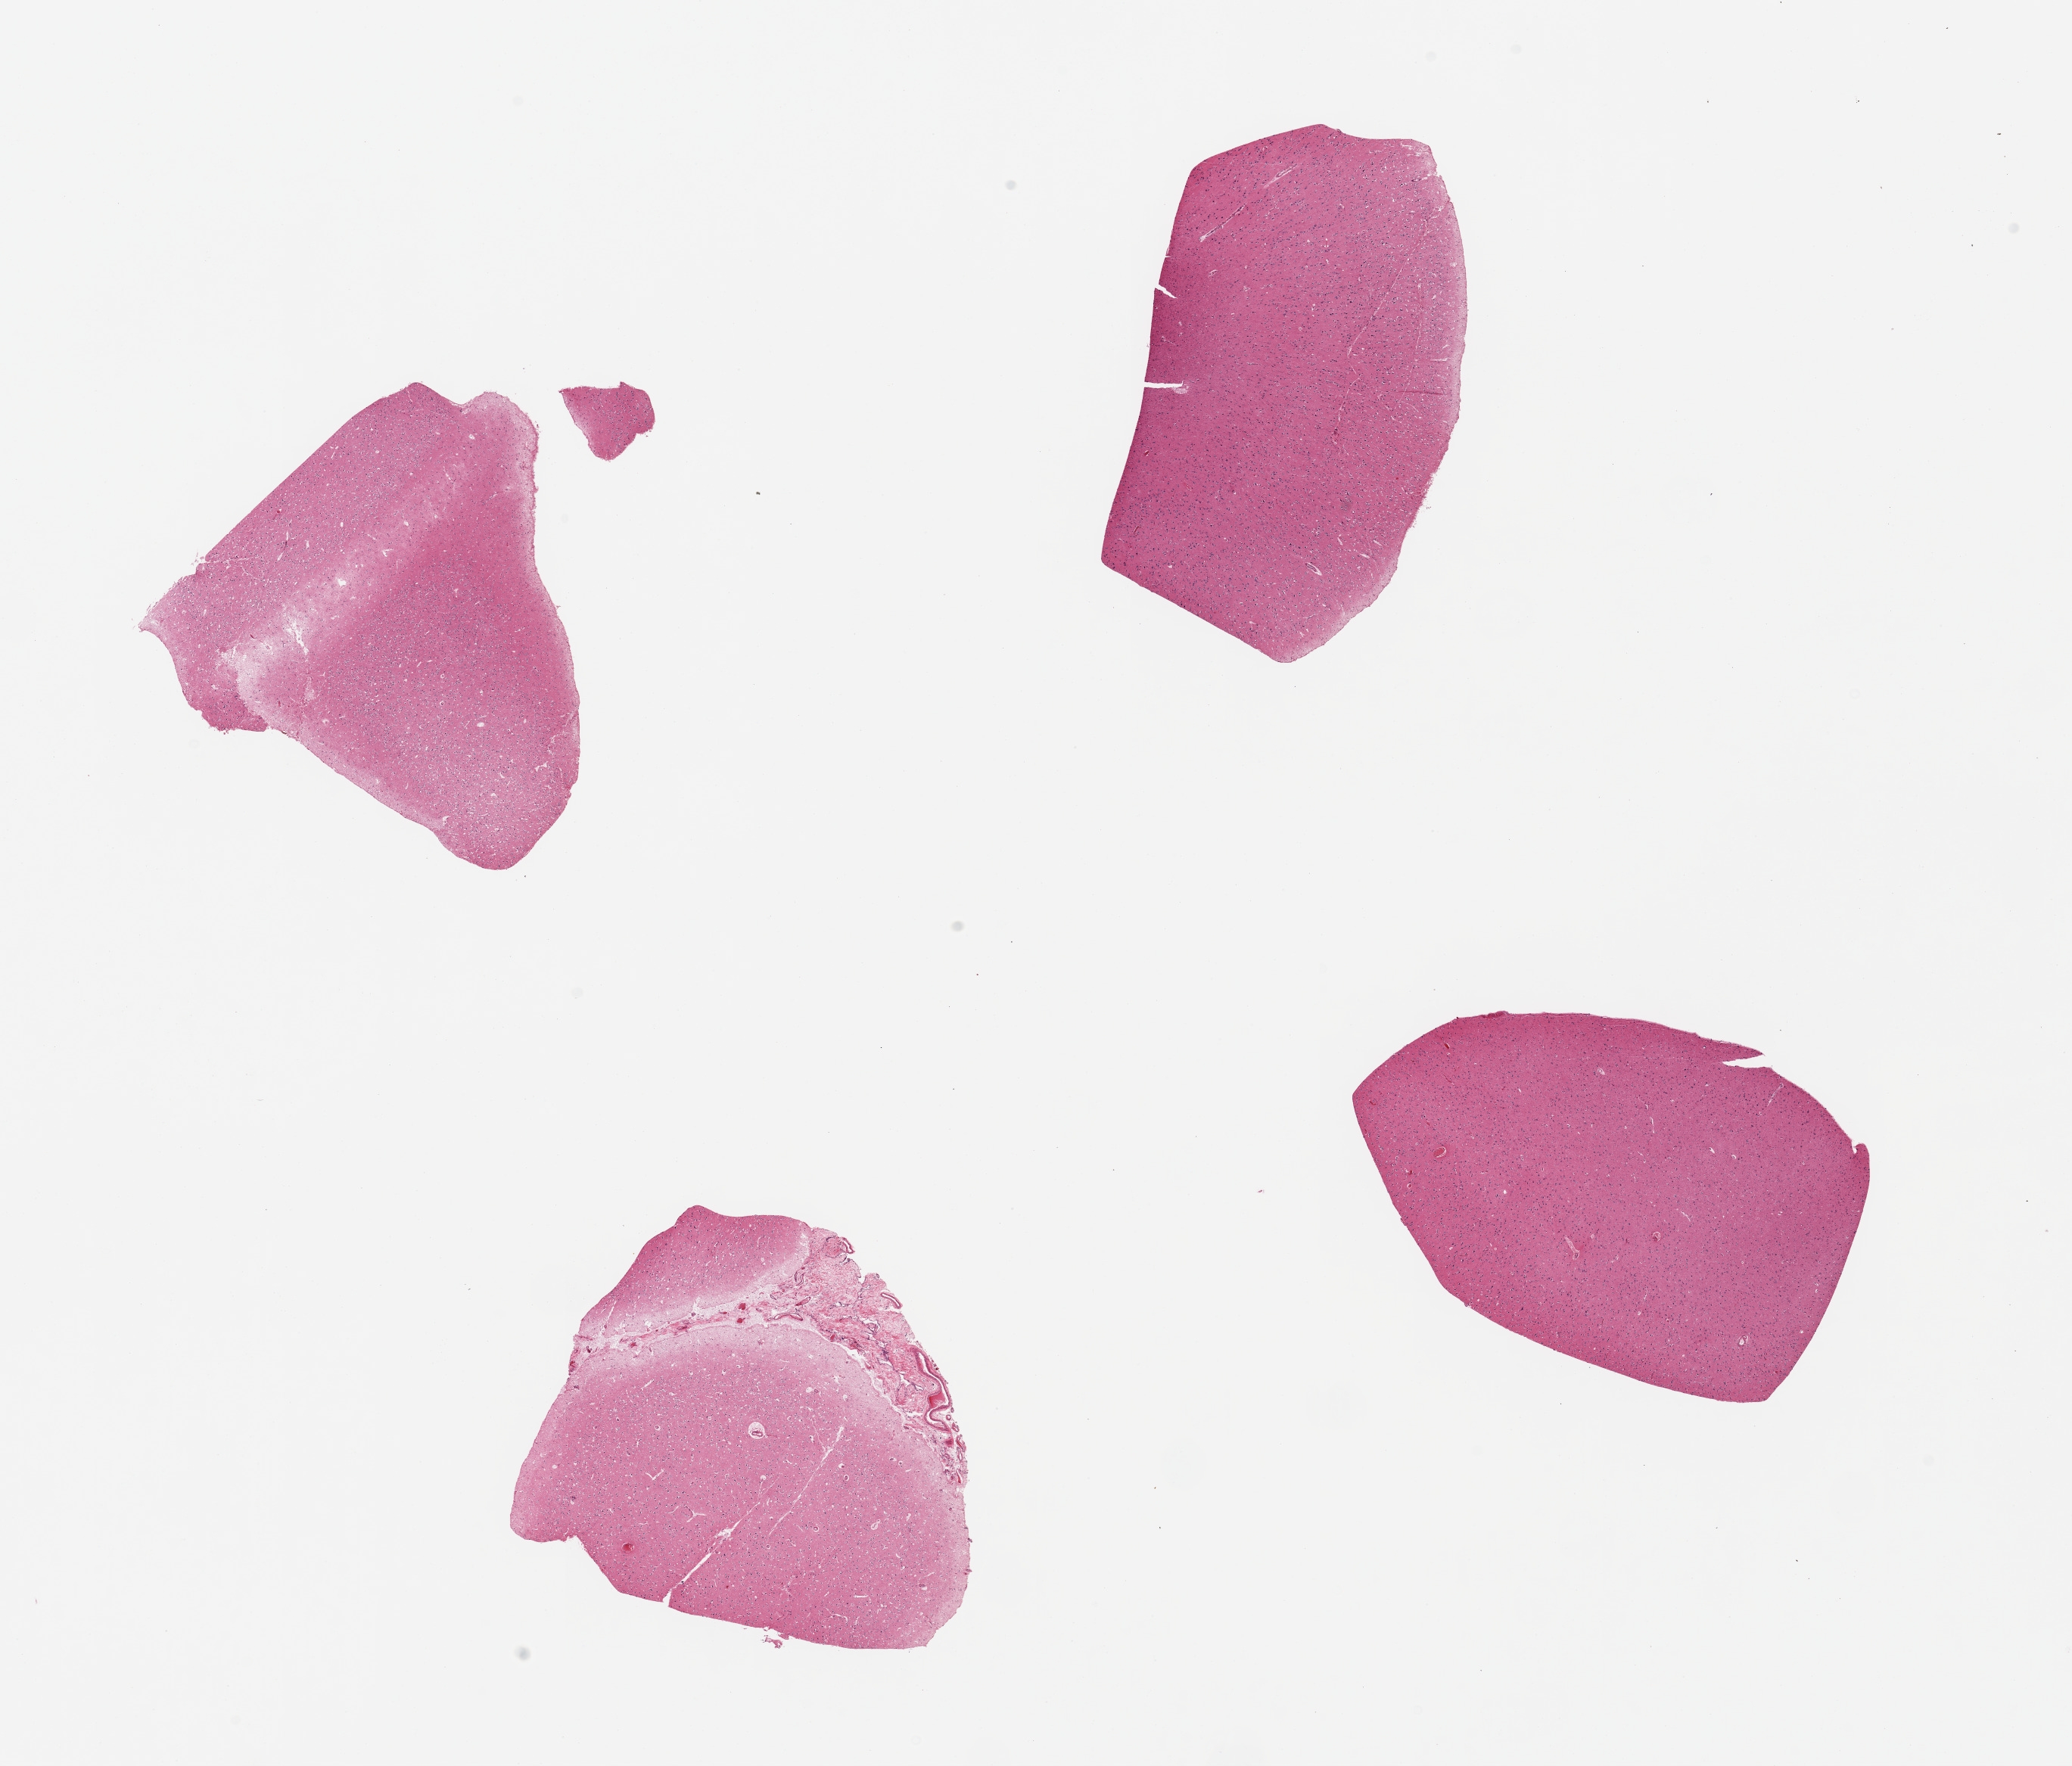
Digitized H&E-stained section, brightfield — low-resolution overview of the scanned area, about 21.7 x 18.5 mm (from a 20x scan). PAXgene-fixed paraffin-embedded (PFPE) section. Target tissue: cerebral cortex. Tissue donor sample.
- review note (as recorded): 4 pieces; adherent meninges on 1 piece